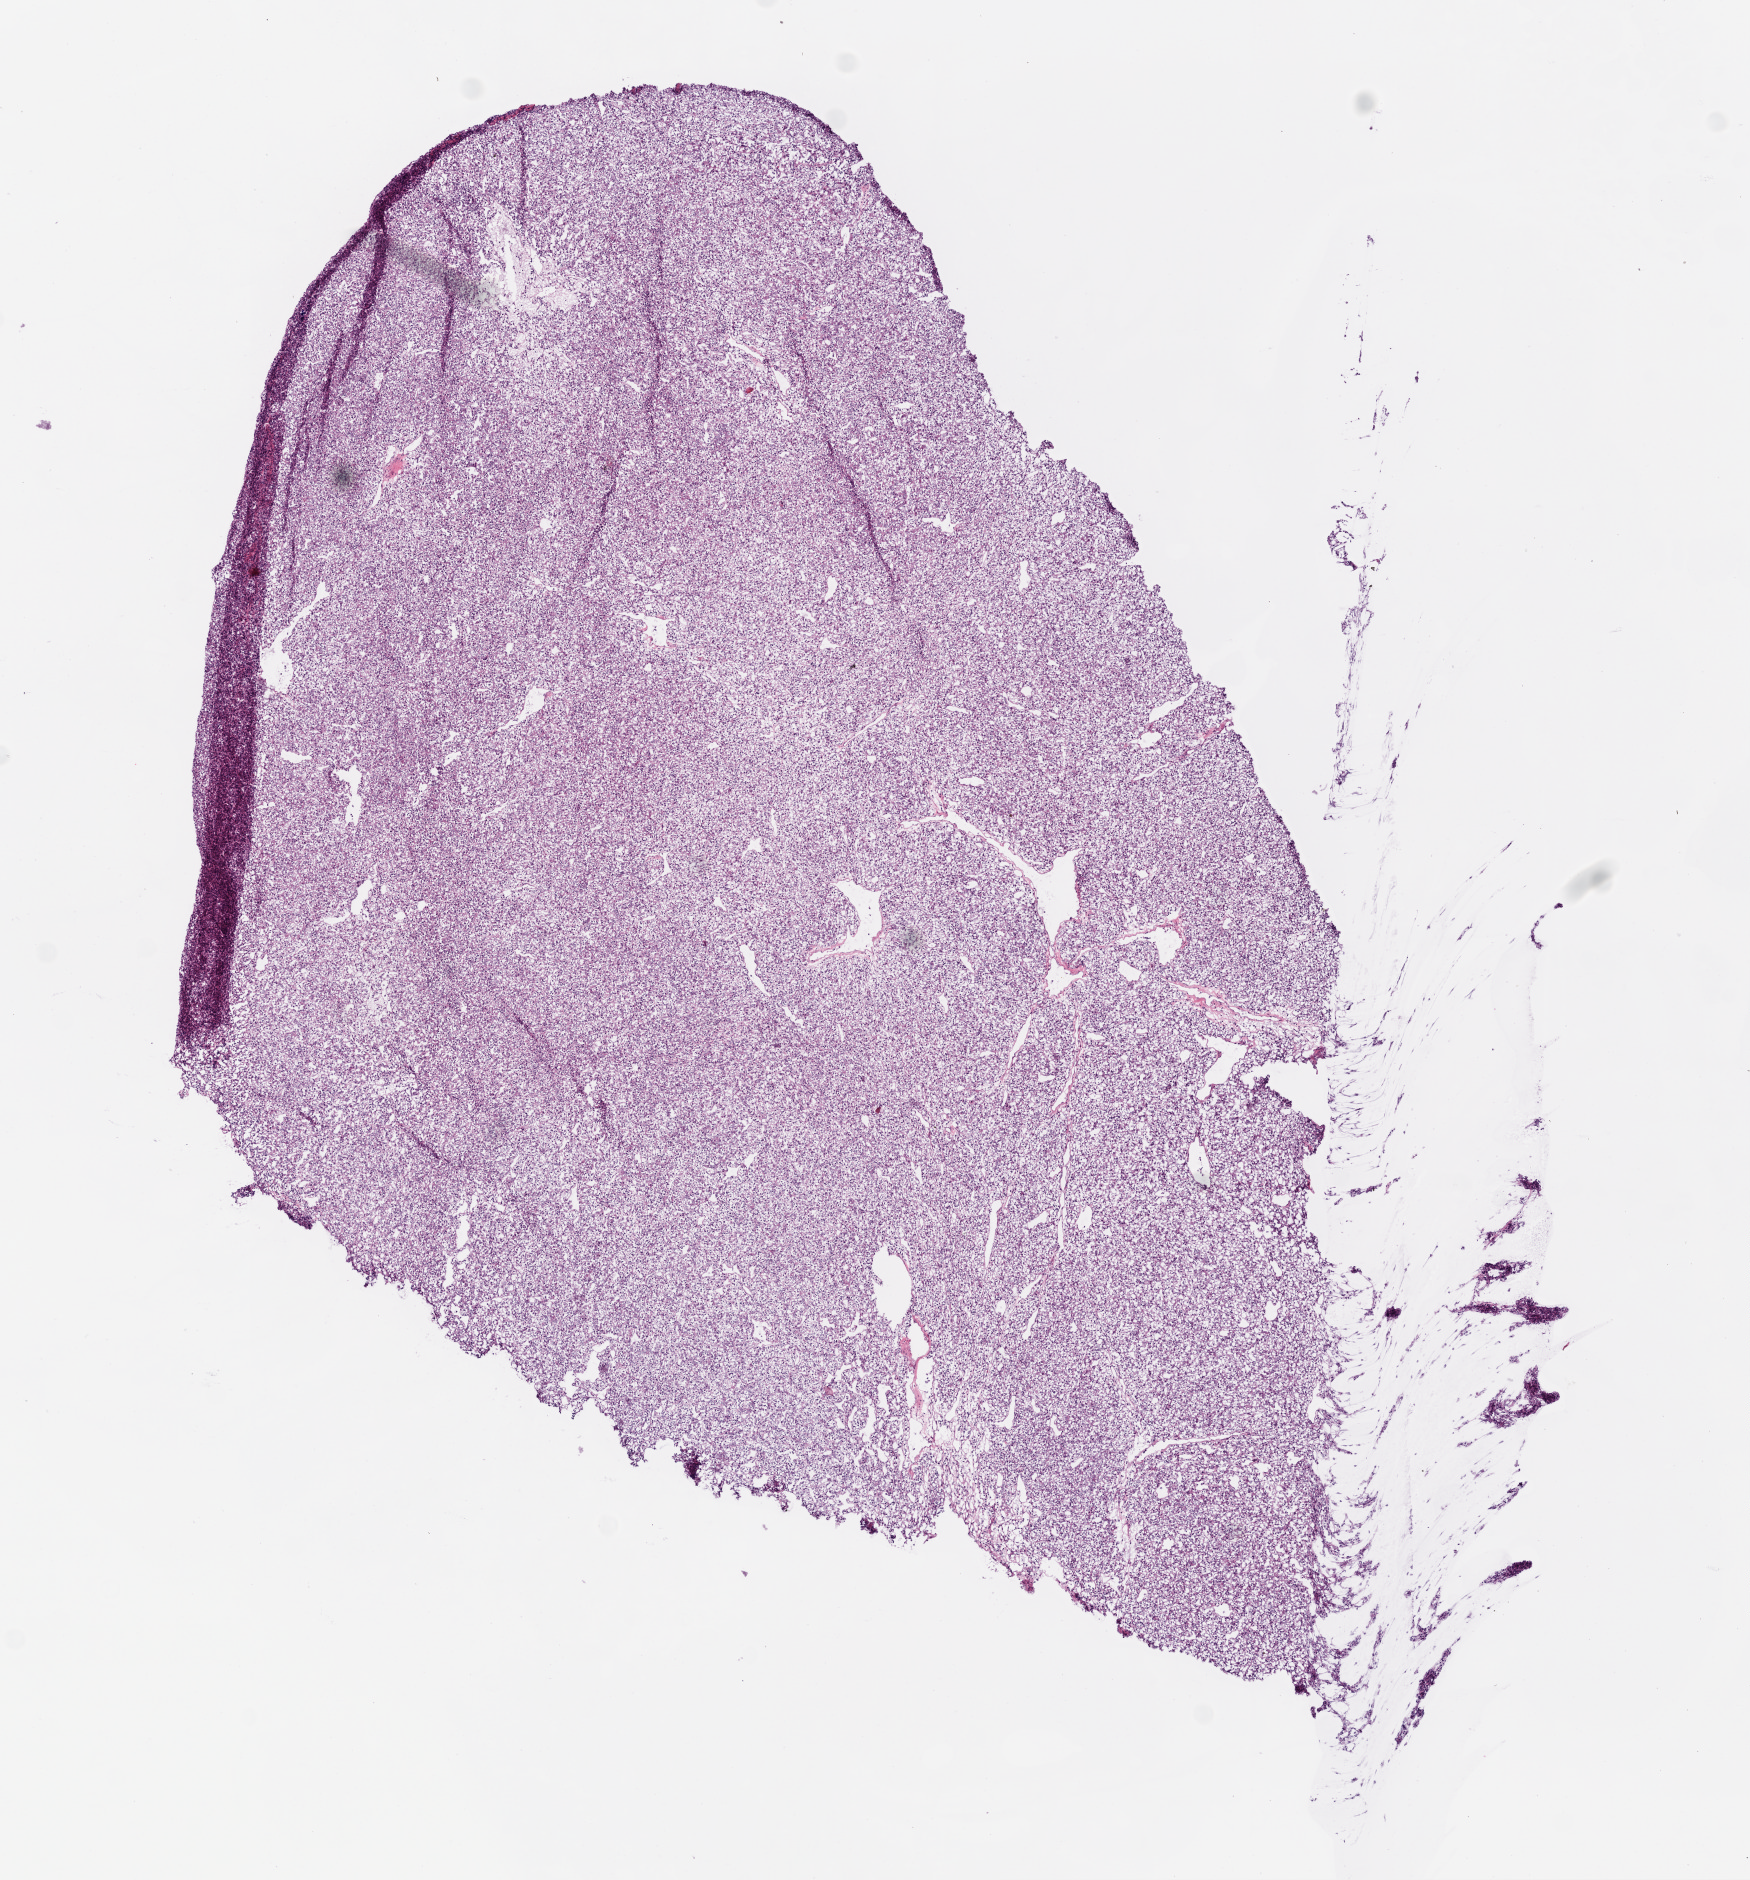
Whole-slide histology image, H&E-stained, shown as a low-resolution overview of the whole scanned area (about 7.0 x 7.5 mm, acquisition: 20x scan), frozen section from the top of the tissue portion, sample: primary tumour, kidney. Female patient; age at initial diagnosis 63 years. Histologic grade: G3 (poorly differentiated). Slide review estimates, as recorded: tumour cells 90%, tumour nuclei 90%, normal cells 0%, stromal cells 10%, necrosis 0%.
* TNM: T1a N0 M0
* laterality: left
* AJCC pathologic stage: I (6th edition)
* histologic diagnosis: Clear cell adenocarcinoma, NOS